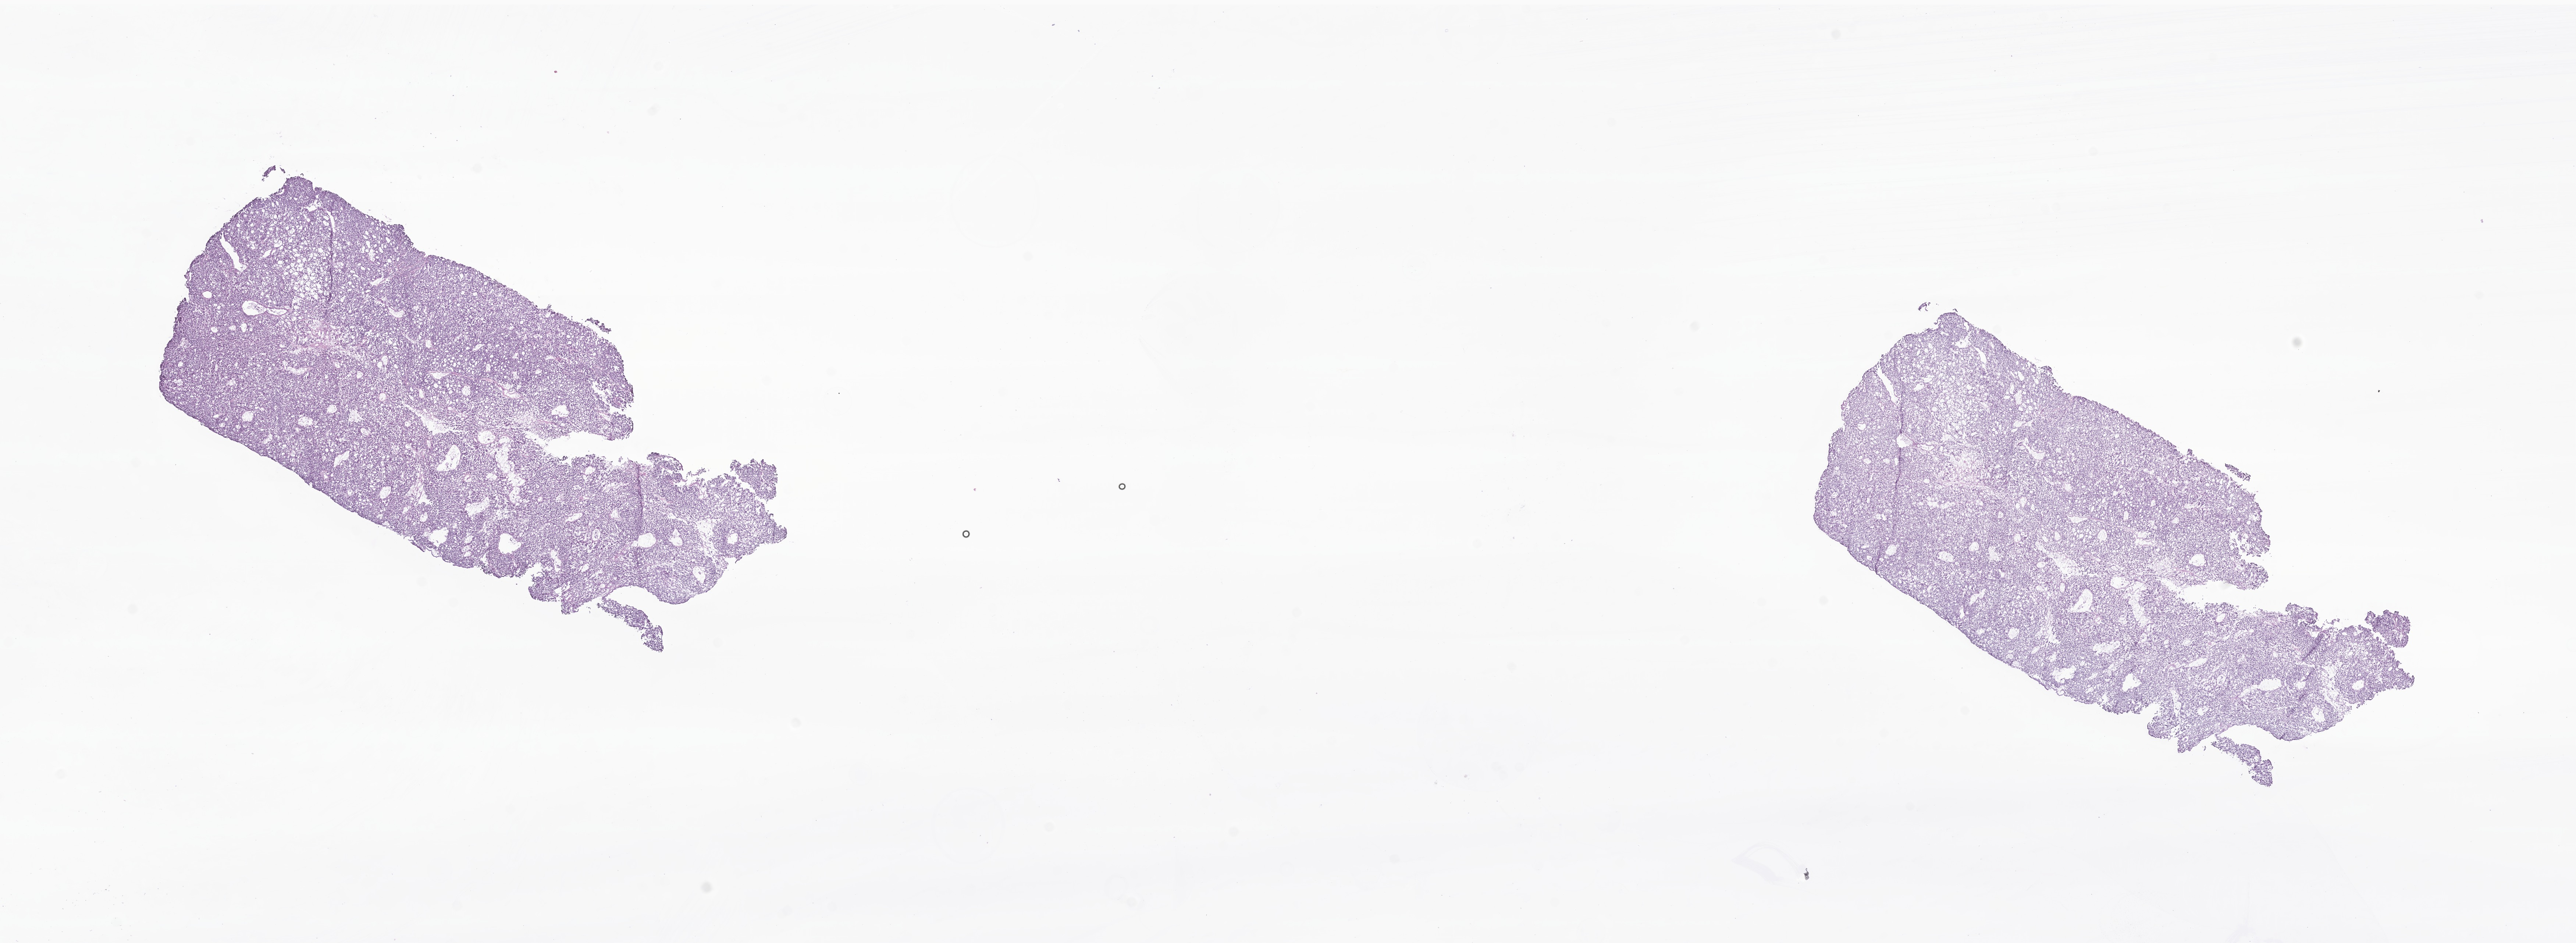
Digitized hematoxylin and eosin (H&E)-stained section of tumor tissue from the thyroid — shown as a low-resolution overview of the whole scanned area (about 29.5 x 10.8 mm). Cryosection (OCT / tissue freezing medium). Patient female; age 213 months (17 years 9 months).
Diagnosis (ICD-O-3 morphology term): Papillary carcinoma, follicular variant.